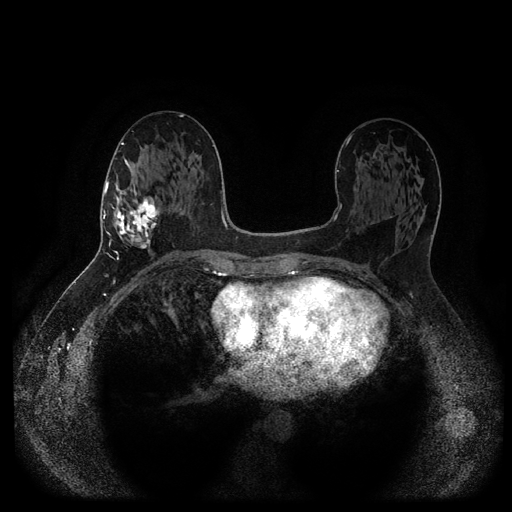
Breast MRI (dynamic contrast-enhanced, multi-phase), one axial slice. Position 50 of 116 along the scan axis. Dynamic contrast-enhanced series, time point 2 of 5 at this slice position (early post-contrast). 1.5 T. TE 2.6 ms, TR 5.3 ms. 2 mm slice thickness. 512 × 512 image matrix. Female patient, age 58 years.
Outlined on this slice (semi-automatic segmentation, software-assisted and operator-edited):
- breast lesion (labelled 'tumour' in the annotation; benign lesions carry a separate 'benign' label): bounding box [x1, y1, x2, y2] px = [111, 189, 161, 253]